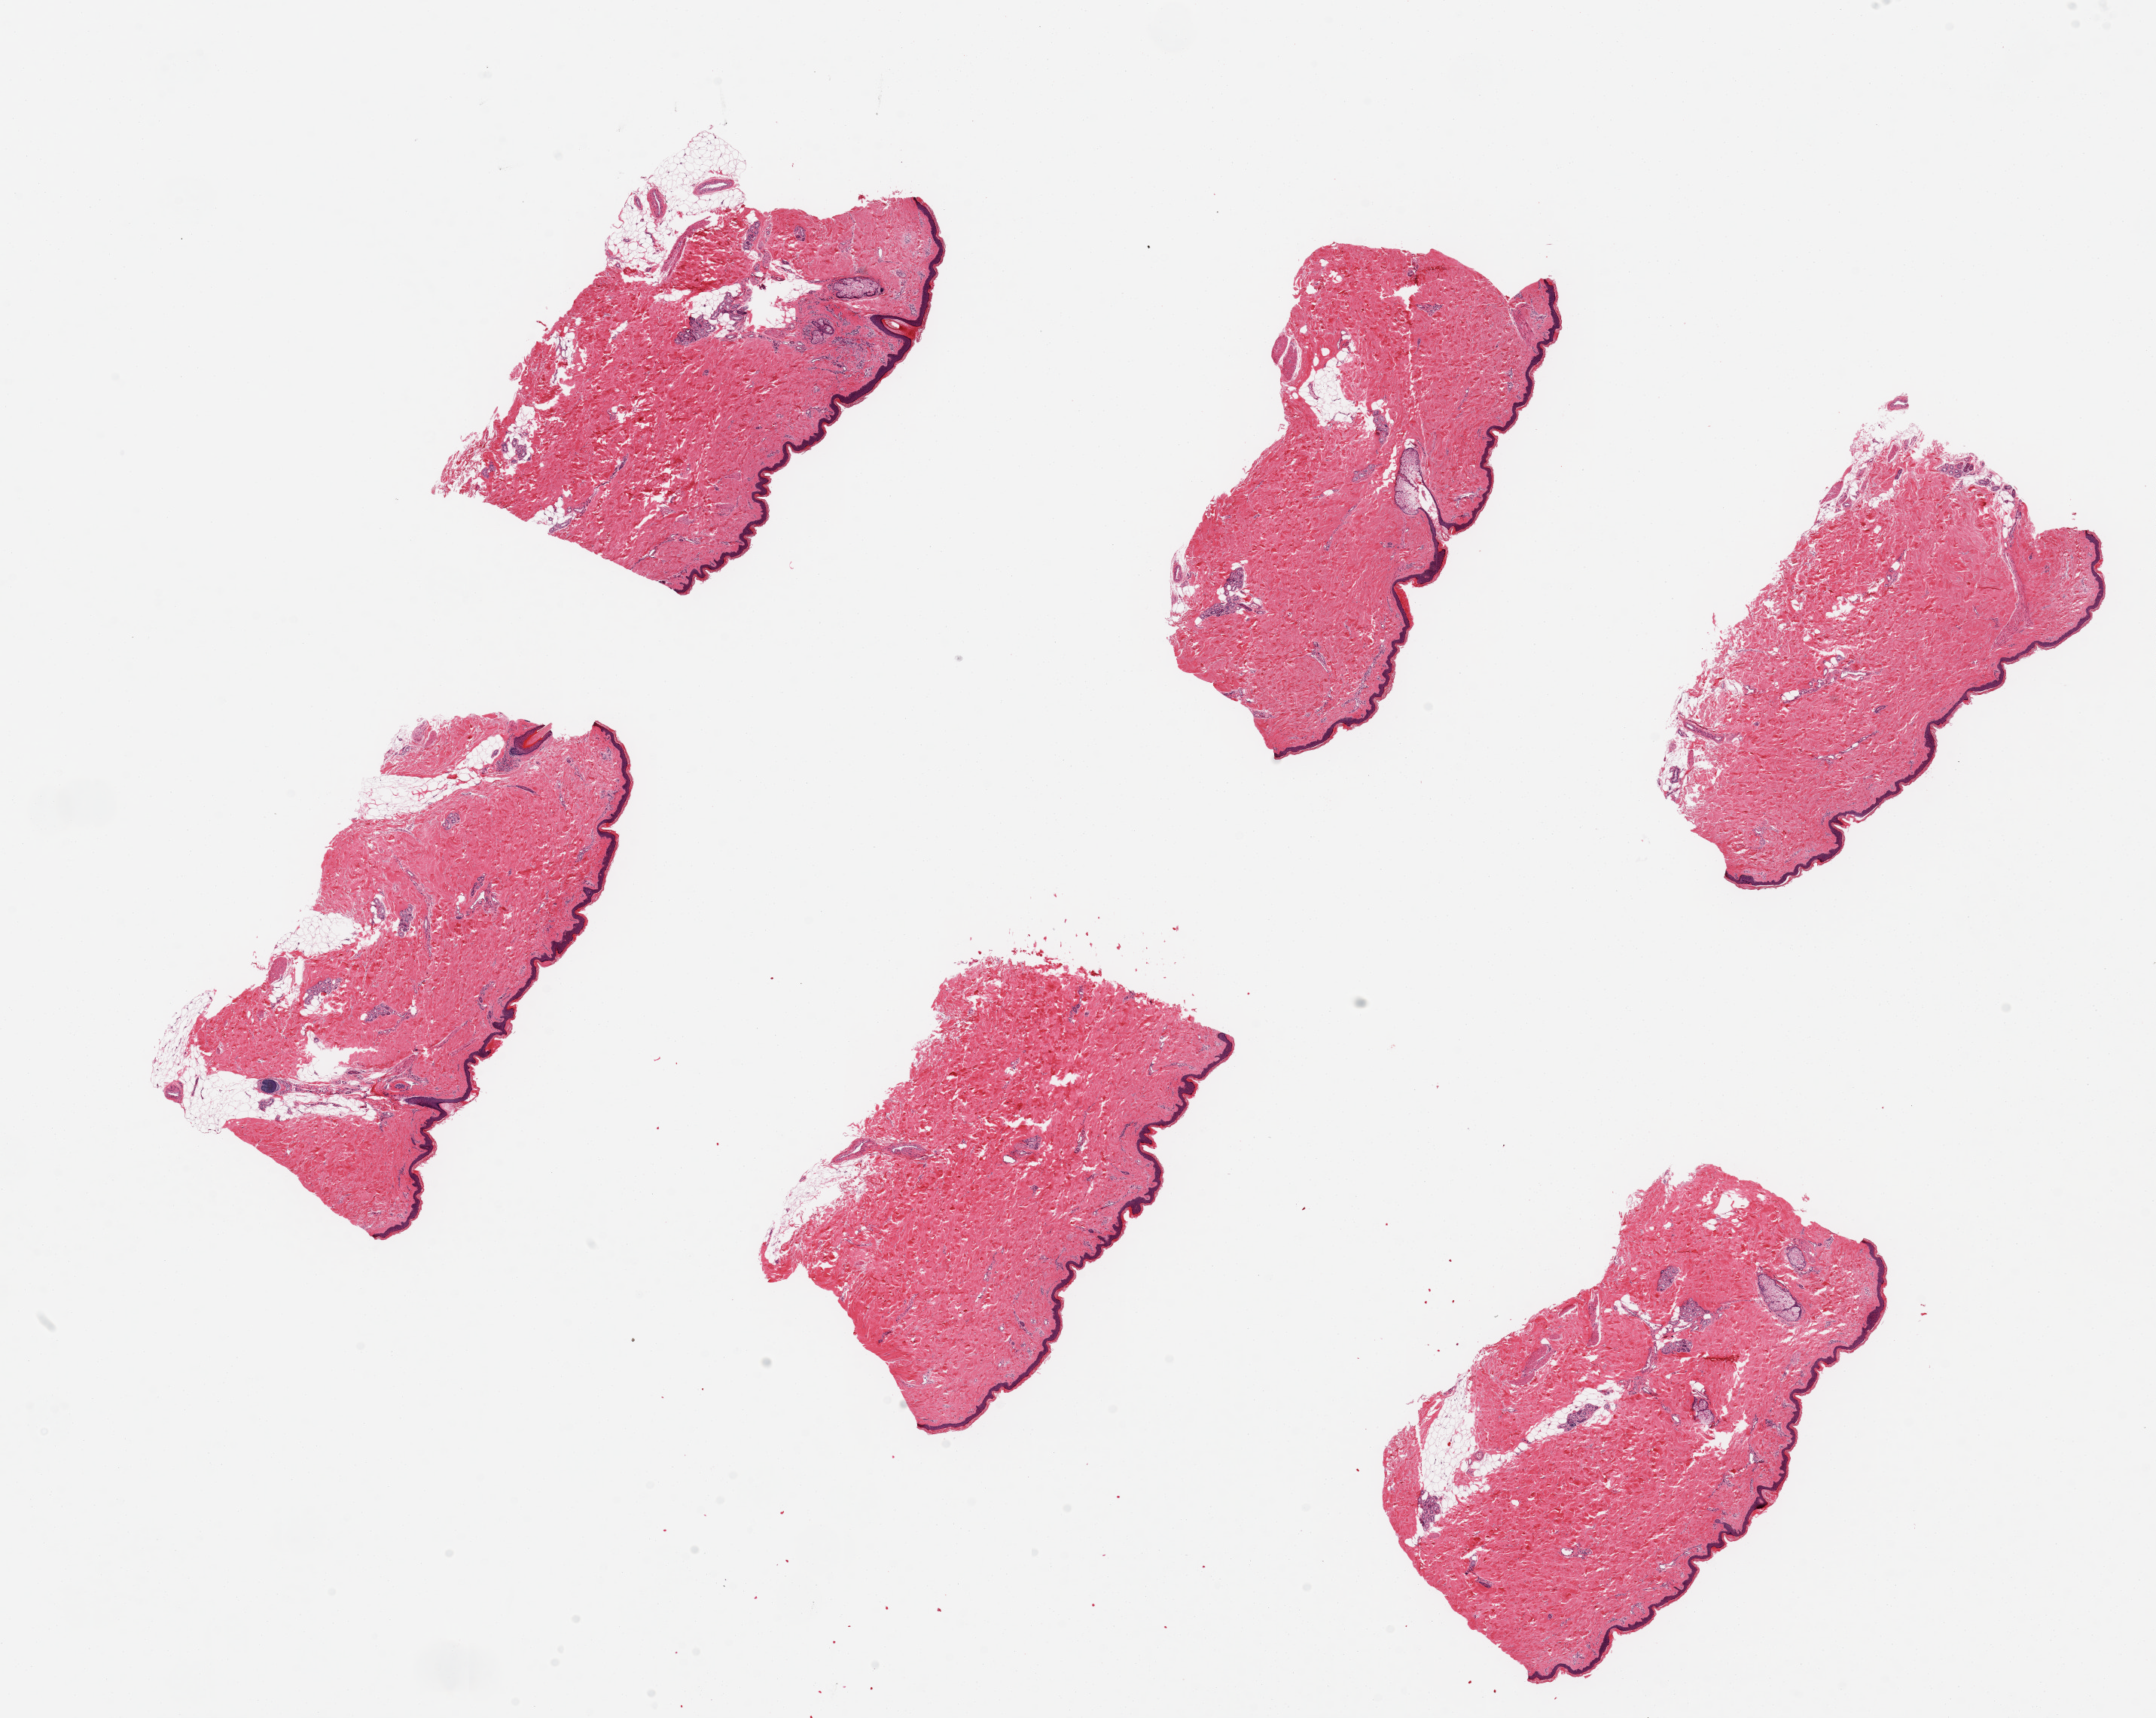
Whole-slide image, H&E stain — whole scanned area (about 22.6 x 18.0 mm) shown as a low-resolution overview, PAXgene-fixed paraffin-embedded (PFPE) section, target tissue: skin of lower leg, donor tissue sample. Donor: male.
Review note (as recorded): 6 pieces up to 6x3 mm; minimal subcutaneous adipose.